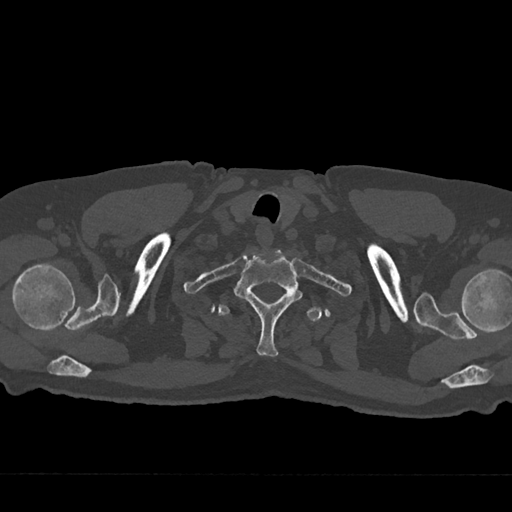
CT including the spine, one axial slice. Position 654 of 797 along the scan axis. Reconstruction kernel Br40s/3. Bone window (W 1800 / L 400 HU). 0.5 mm slice thickness. 512 × 512 image matrix, field of view 377 × 377 mm. Patient: male, 75 years. Case-level facts recorded for this patient, not image findings: primary cancer: renal; vertebrae with lytic lesions (as recorded): T4.
Structures marked on this image (semi-automatically segmented with operator editing):
- T1 vertebra: bounding box <234,250,304,357> (left, top, right, bottom; pixels)
- T2 vertebra: <218,291,322,321>